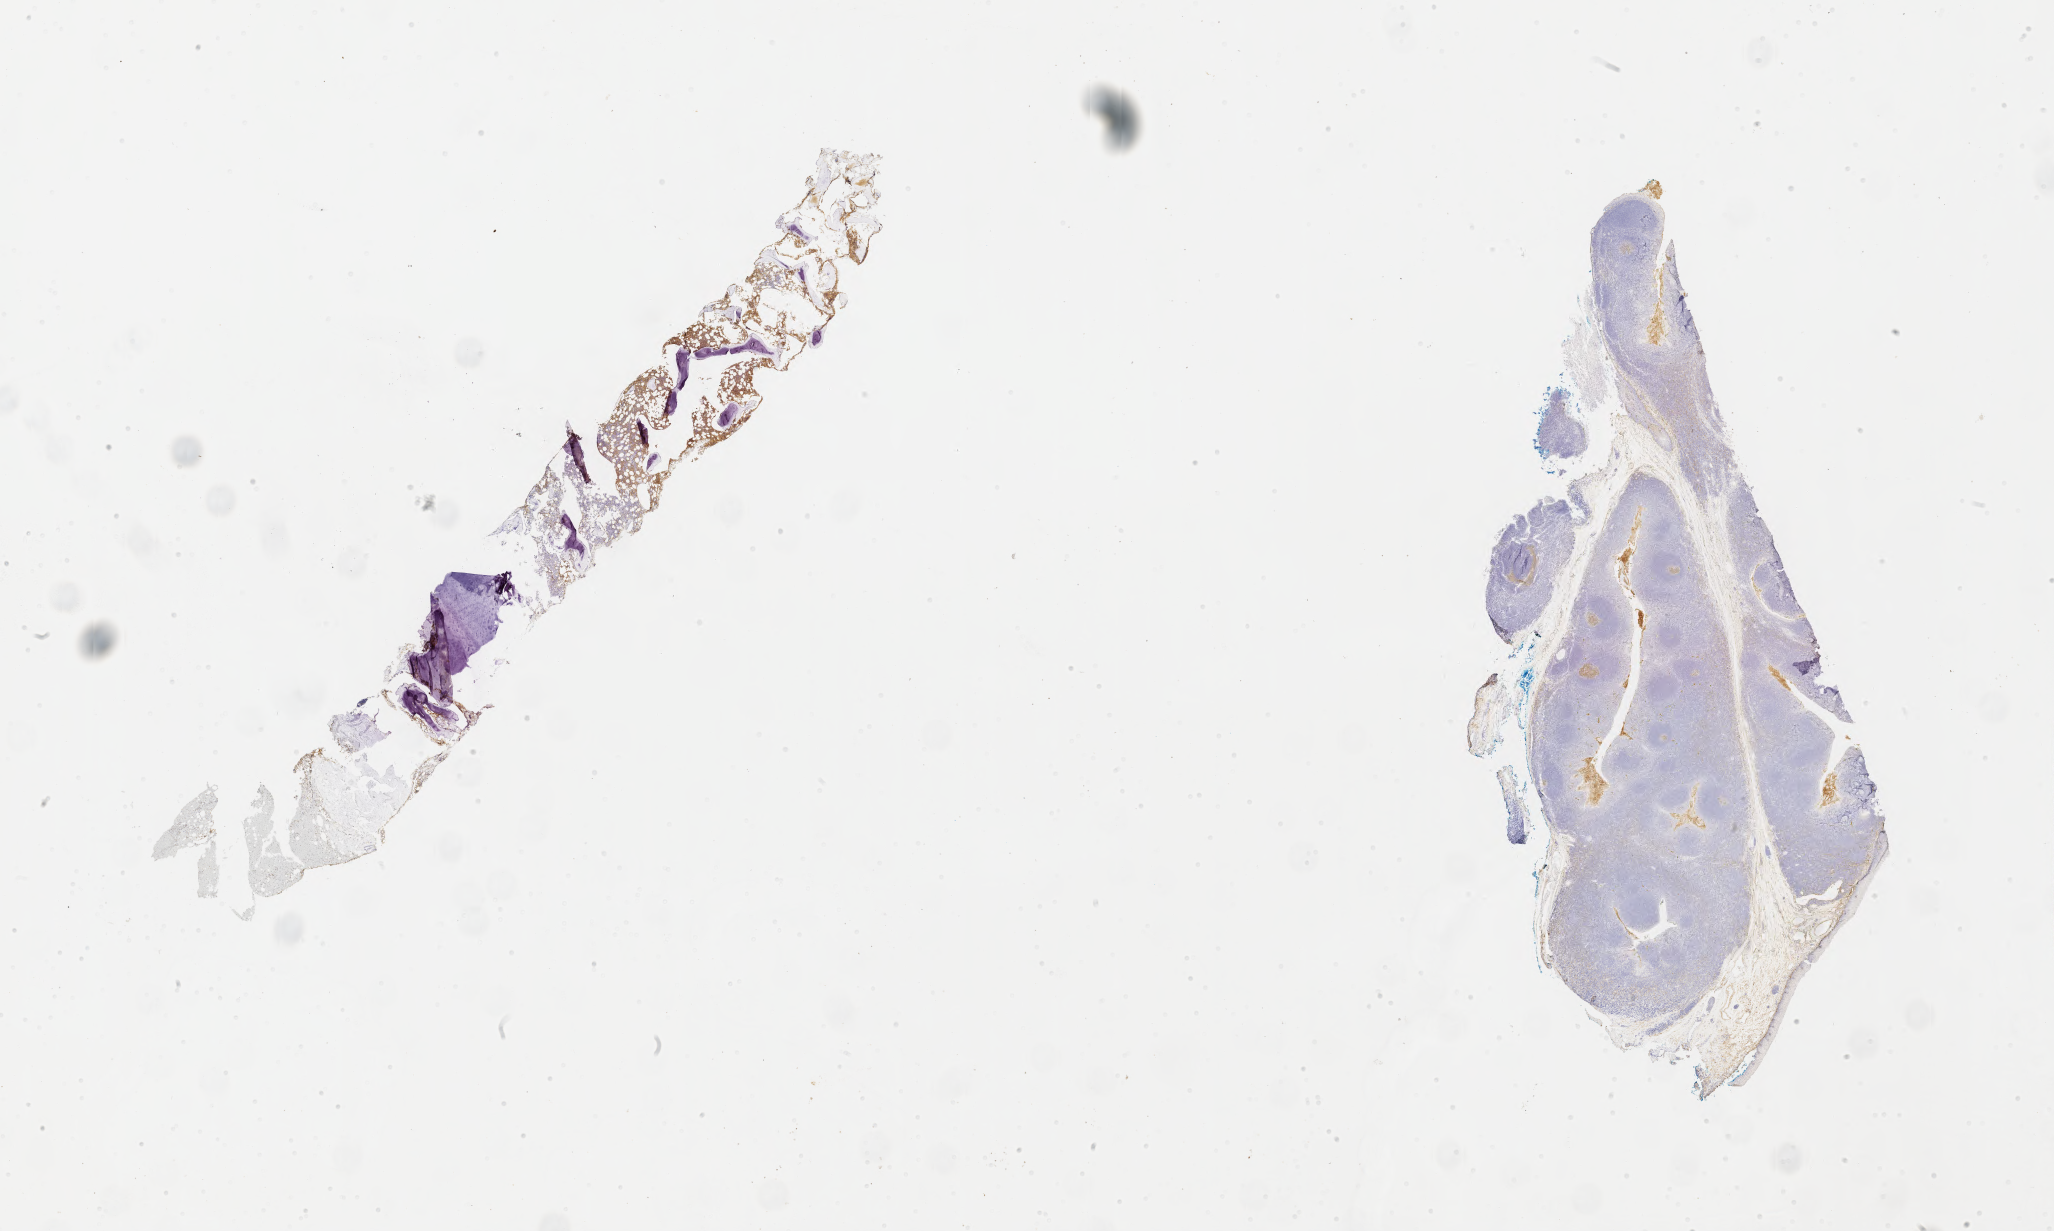
Immunohistochemistry (IHC) whole-slide image stained for CD10 — whole scanned area (about 33.2 x 19.9 mm) shown as a low-resolution overview, tumor tissue, site: bone marrow. Male patient, aged 15.
Diagnosis: Burkitt lymphoma, NOS.